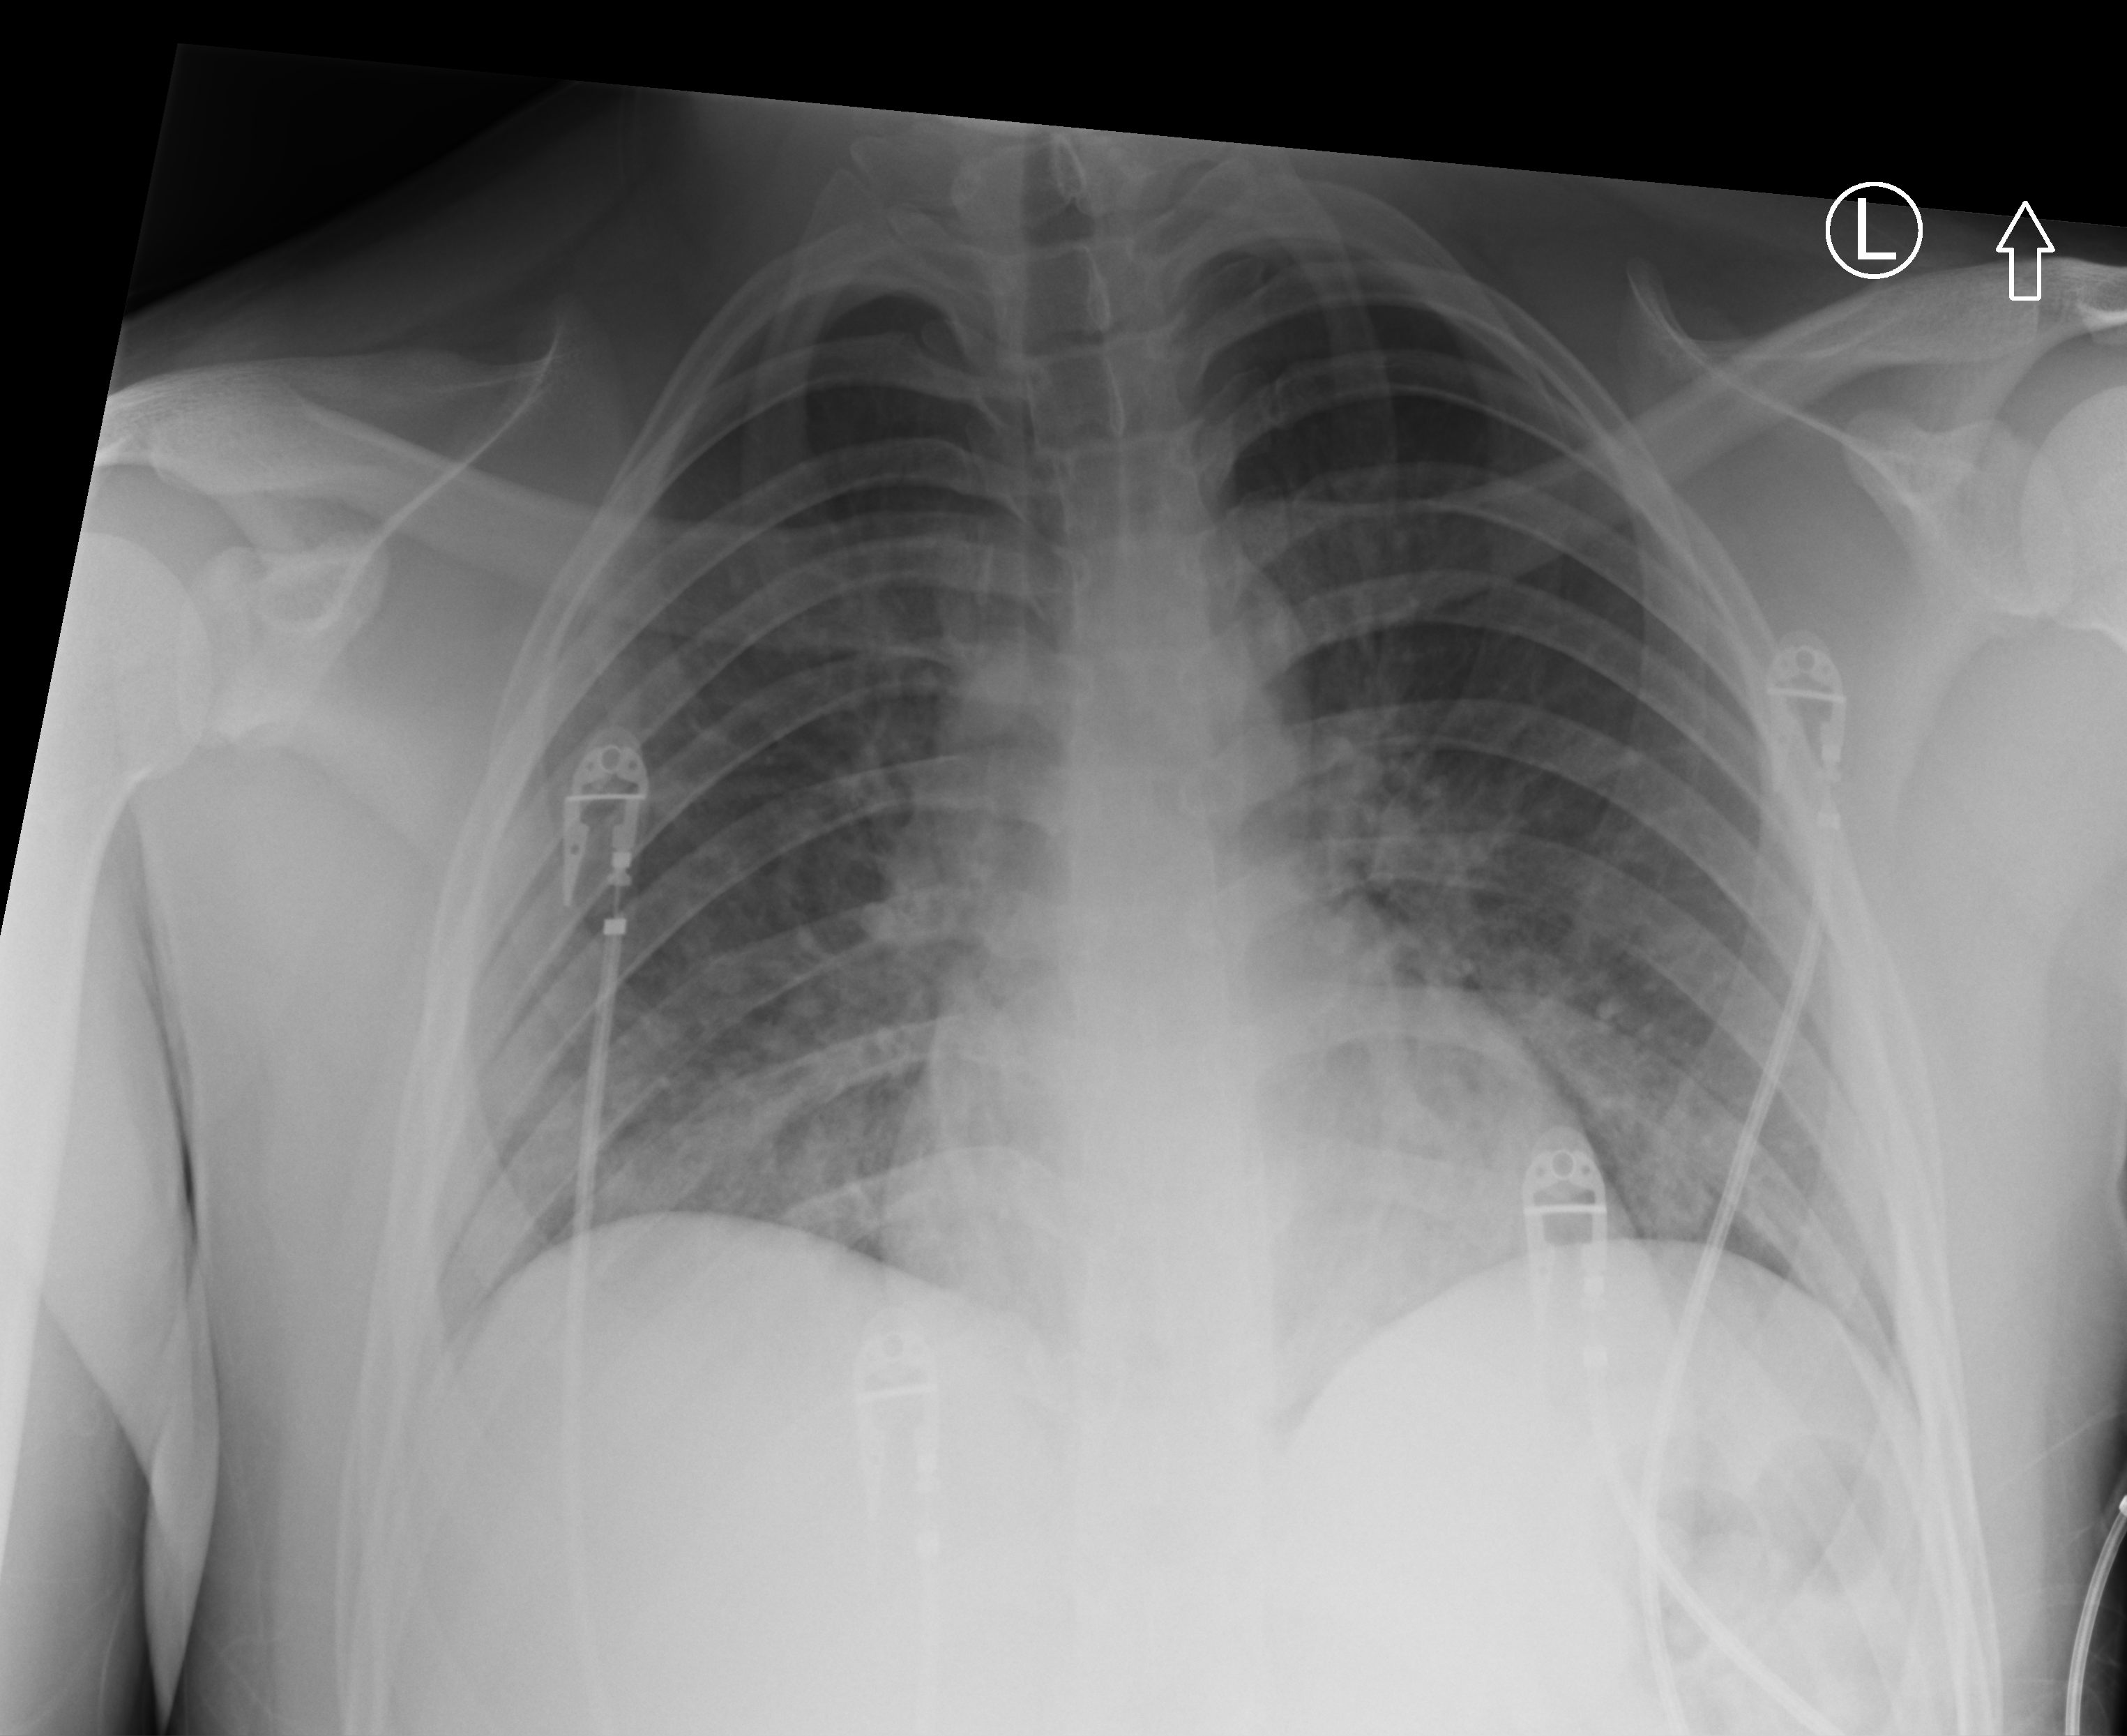
Portable chest radiograph; anteroposterior (AP) projection. Patient hospitalised with COVID-19; male, aged 18–59 years.
From the hospital-stay record, not from the radiograph (when in the stay this image was taken is not recorded): chronic kidney disease (admission record): no; admitted to intensive care during this hospital stay: no.